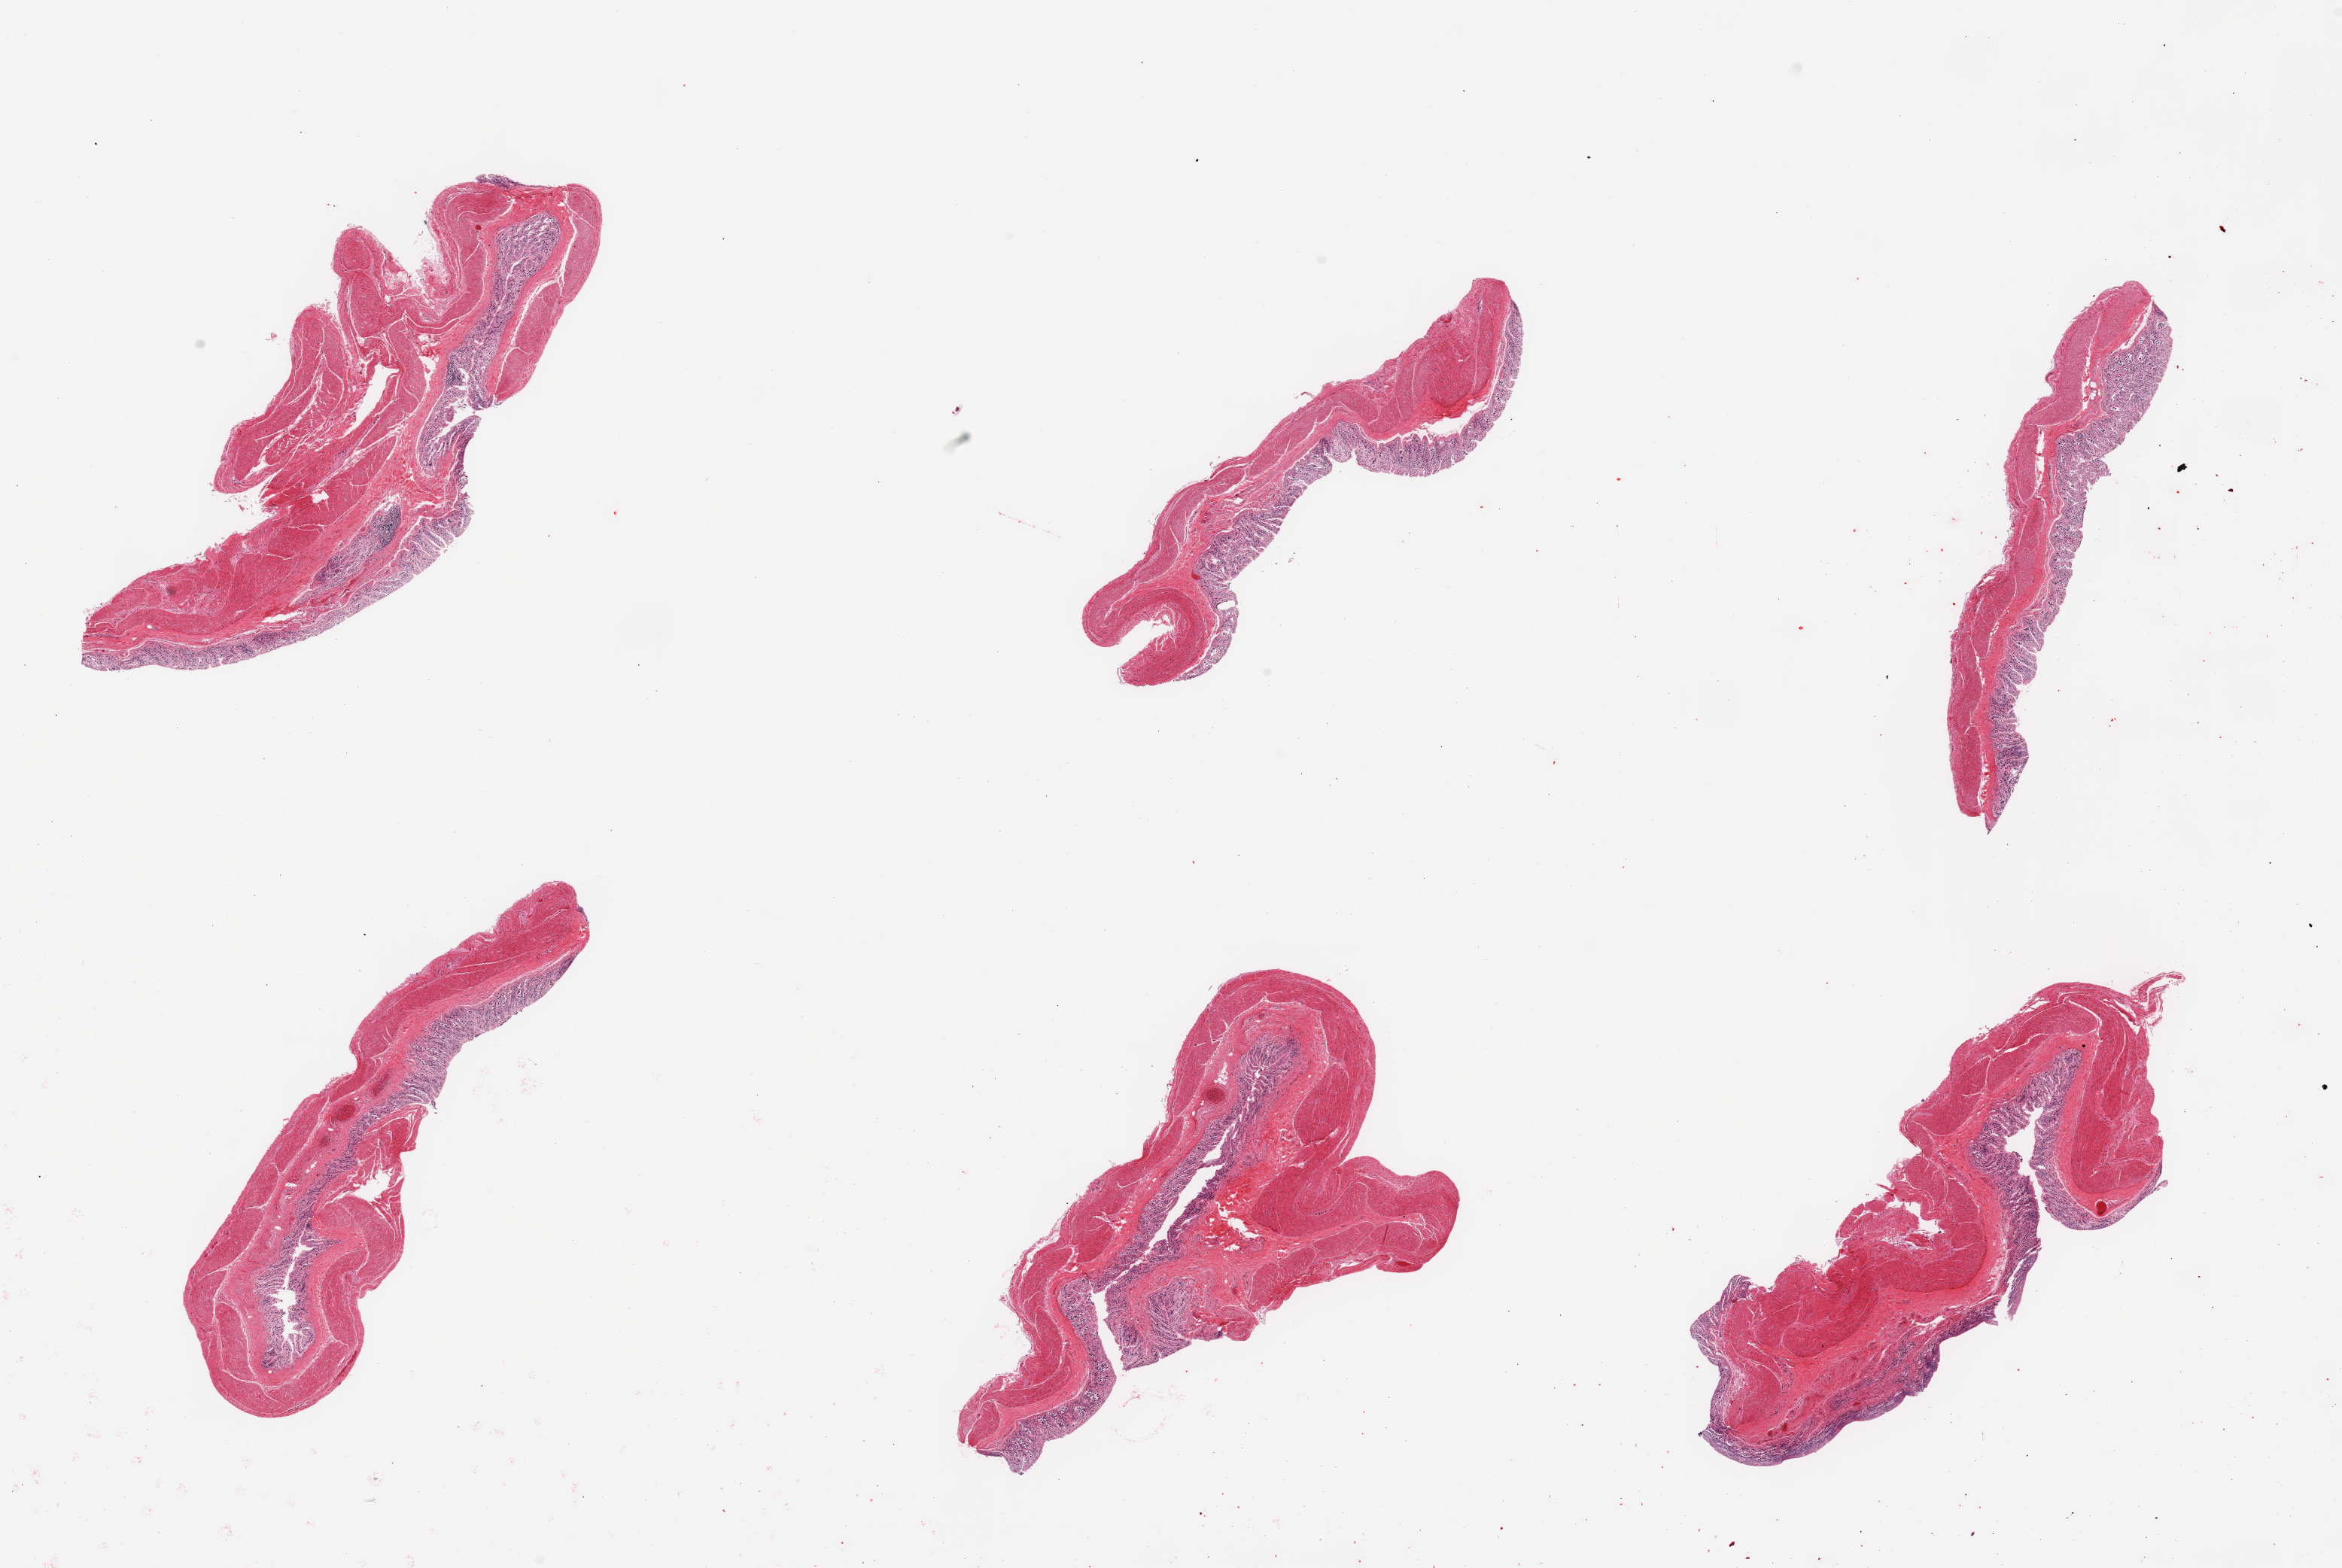
Whole-slide image, H&E stain, brightfield — shown as a low-resolution overview of the whole scanned area (about 24.6 x 16.5 mm). PAXgene-fixed, paraffin-embedded tissue. Target tissue: transverse colon. Donor tissue sample. Donor sex: female.
* pathologist's review note for this sample: 6 pieces; mucosa totally autolyzed; muscularis moderately autolyzed